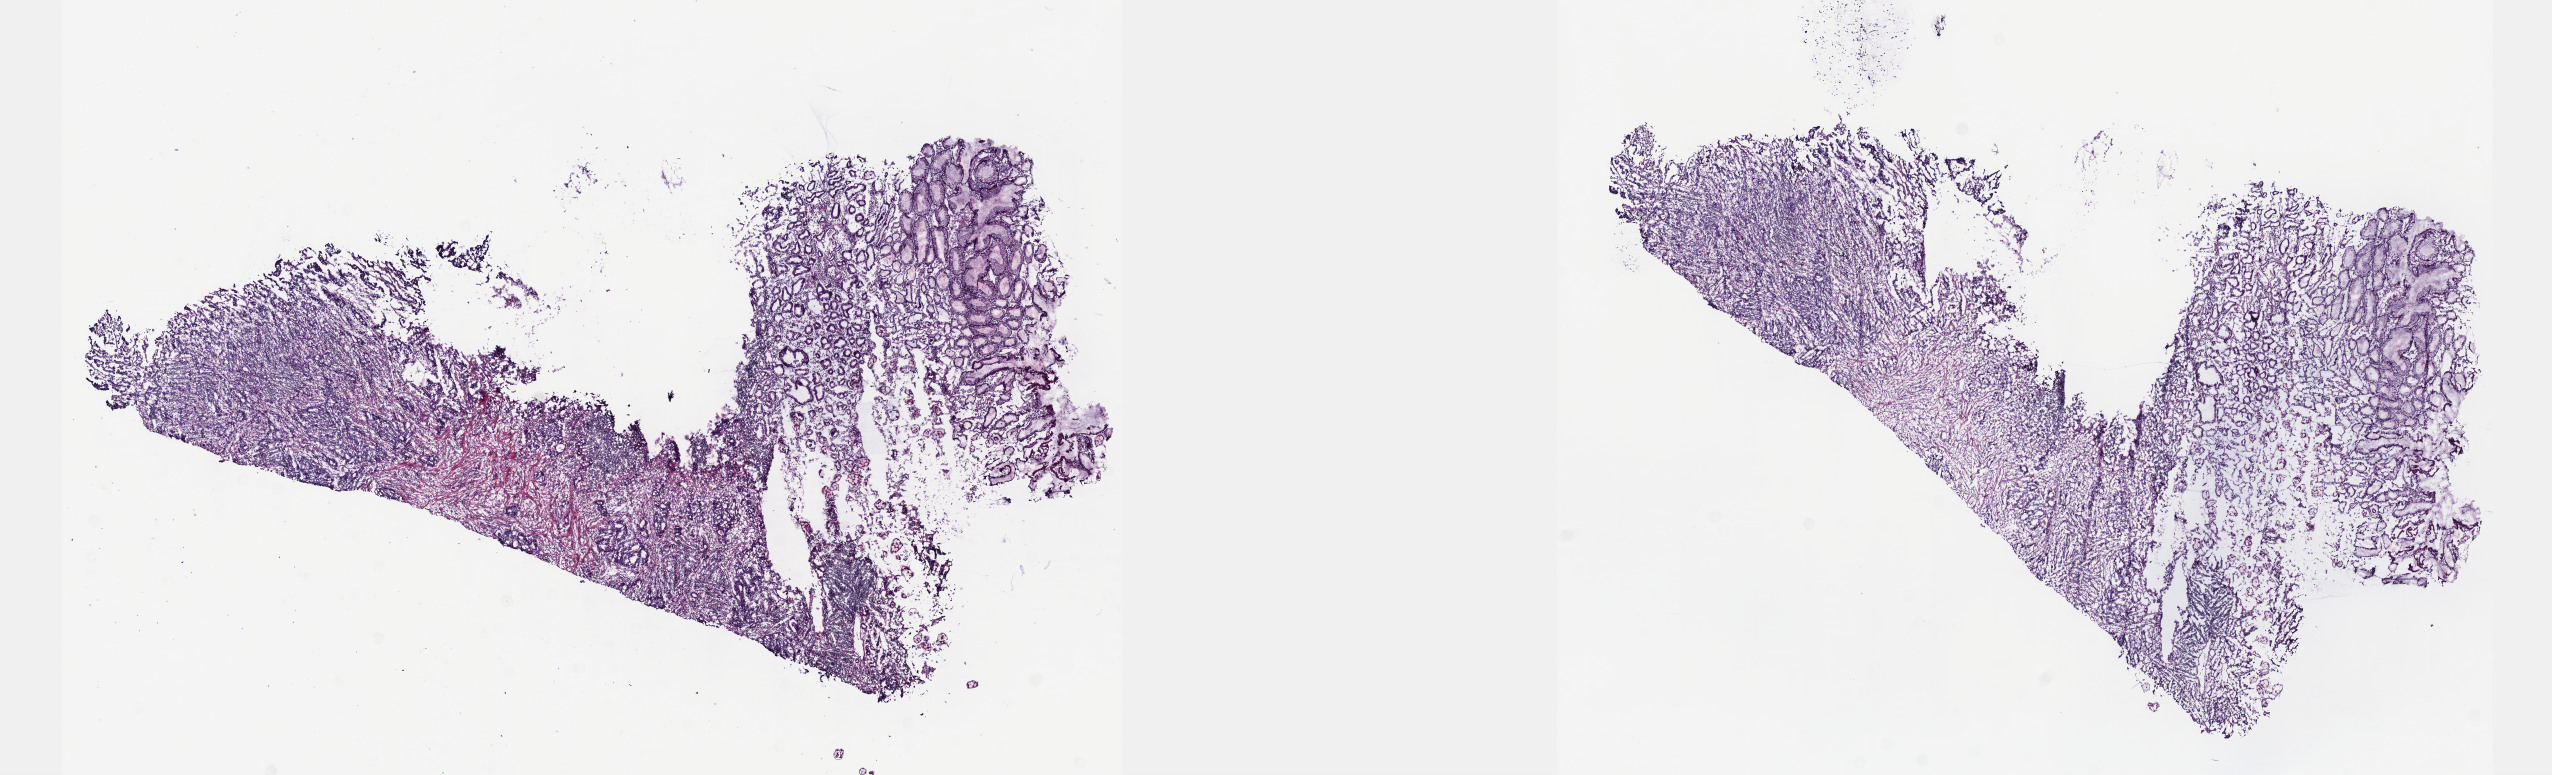
Whole-slide histology image, Hematoxylin and eosin (H&E) stained, a low-resolution overview of the entire scanned area, about 20.6 x 6.3 mm (acquisition: 40x scan). Frozen section from the top of the tissue portion. Sample: primary tumour, stomach. Patient: male, age at initial diagnosis 62 years. Histologic grade: G2 (moderately differentiated). Composition of this section per pathologist review: tumour cells 65%, tumour nuclei 65%, normal cells 7%, stromal cells 28%, necrosis 0%. Infiltration values recorded for this section: lymphocyte infiltration 6%, monocyte infiltration 1%, neutrophil infiltration 3%.
• lymph nodes positive (case pathology): 24 of 33 examined
• histologic diagnosis: Tubular adenocarcinoma (gastric antrum)
• AJCC pathologic stage: IIIB (7th edition)